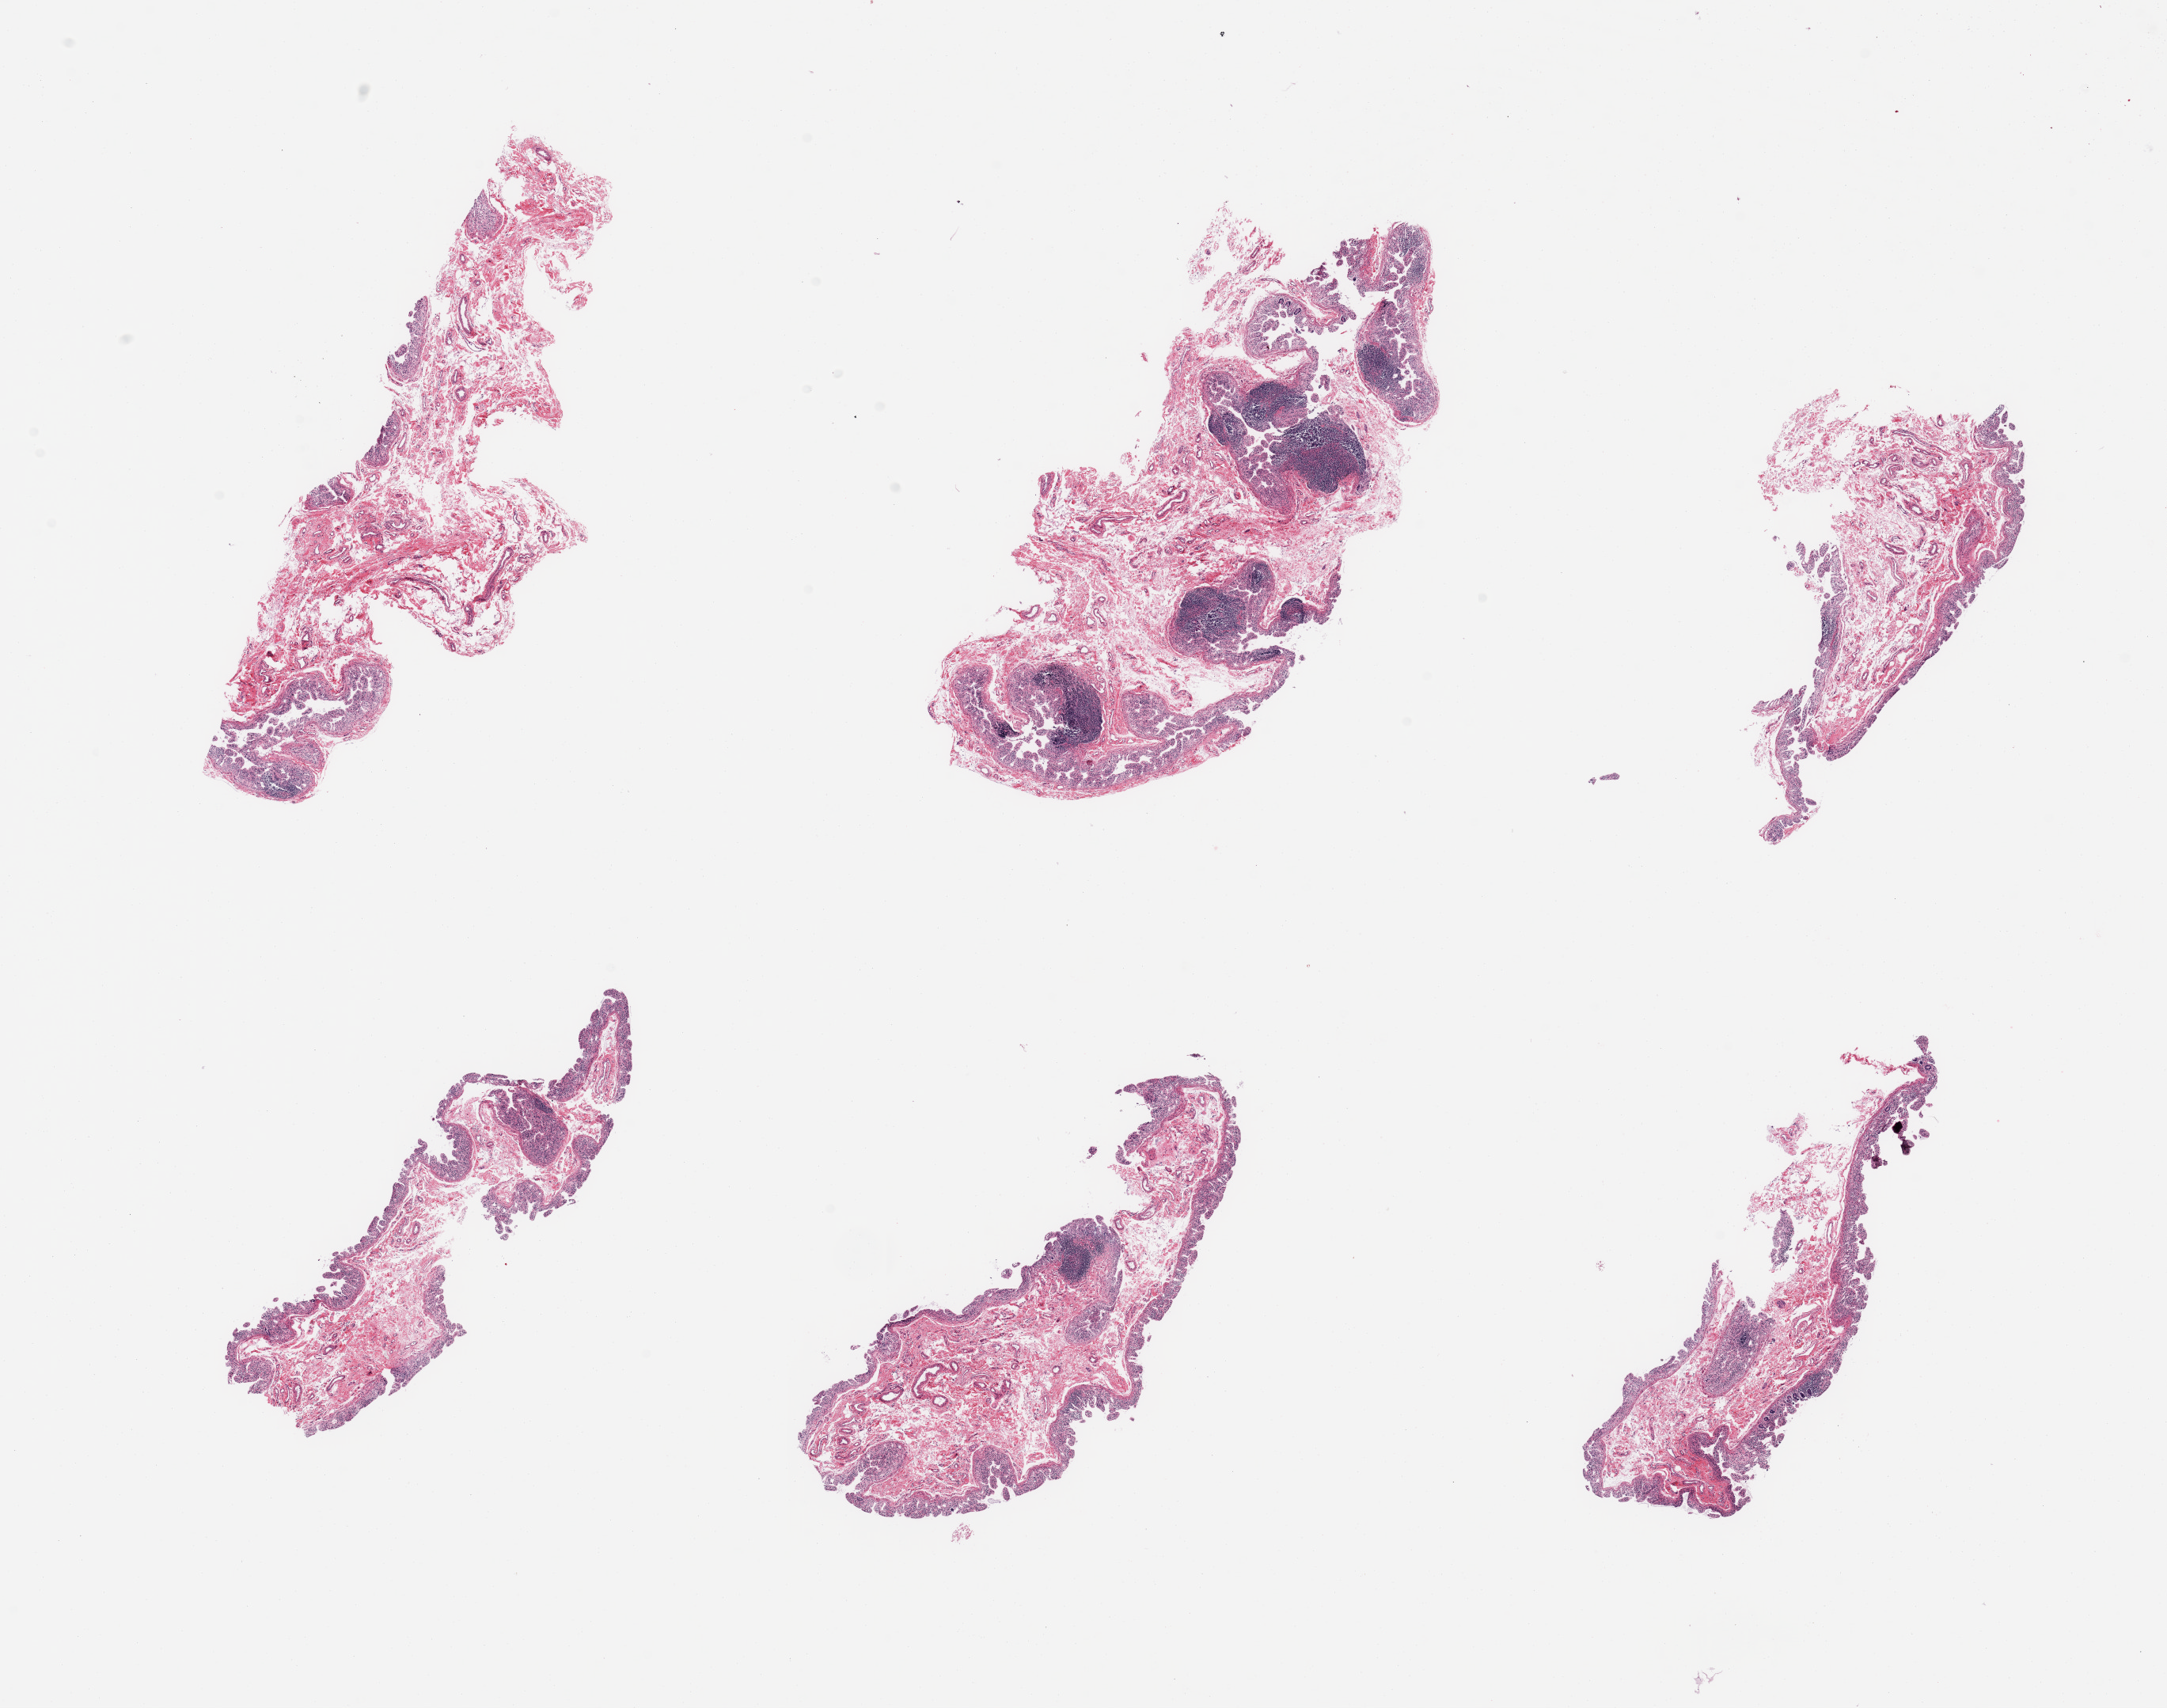
Digitized hematoxylin and eosin (H&E)-stained section, brightfield, low-resolution overview of the scanned area, about 21.7 x 17.1 mm (slide scanned at 20x). Female donor.
- specimen: PAXgene-fixed, paraffin-embedded tissue; sampled site (target tissue): ileum; donor tissue sample